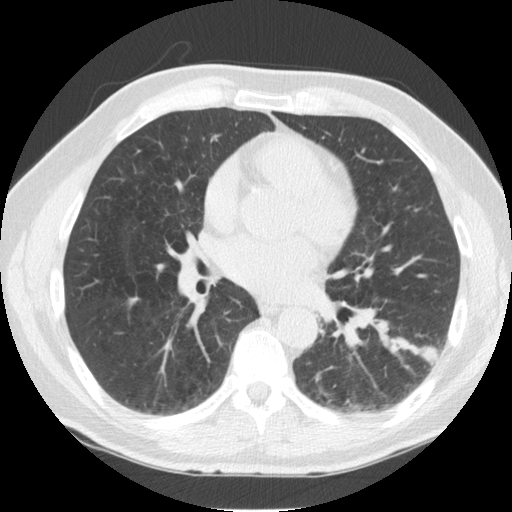
Low-dose screening chest CT, one axial slice. Reconstruction kernel STANDARD. Lung window (W 1500 / L -600 HU). 2.5 mm slice thickness. 512 × 512 image matrix, field of view 344 × 344 mm.
Annotated regions visible in this slice (manually delineated by an expert):
- lesion 1 (tumor, lower lobe of left lung): bounding box (x1, y1, x2, y2) in pixels: (420, 346, 438, 366)